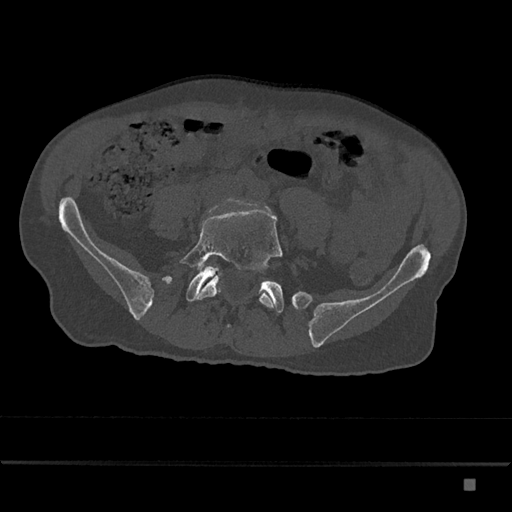
CT including the spine, one axial slice. Position 267 of 797 along the scan axis. Bone window (W 1800 / L 400 HU). 0.5 mm slice thickness. 512 × 512 image matrix, field of view 390 × 390 mm. Patient: male, 72 years. From the clinical record (not read from this slice): primary cancer: prostate.
Annotated regions visible in this slice (semi-automatic segmentation, software-assisted and operator-edited):
- L5 vertebra: box from (x=180, y=209) to (x=283, y=308) px